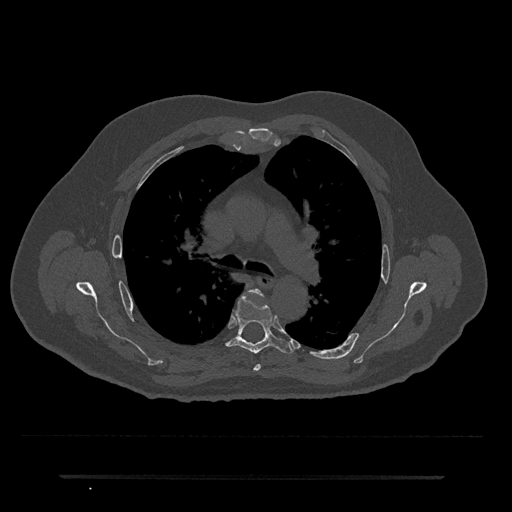
CT including the spine, one axial slice; position 488 of 797 along the scan axis; bone window (W 1800 / L 400 HU); 512 × 512 image matrix. Male patient, age 69 years. From the clinical record (not read from this slice): primary cancer: prostate.
Structures marked on this image (semi-automatically segmented with operator editing):
- T4 vertebra: bounding box (x1, y1, x2, y2) in pixels: (249, 289, 262, 371)
- T5 vertebra: (226, 292, 294, 354)